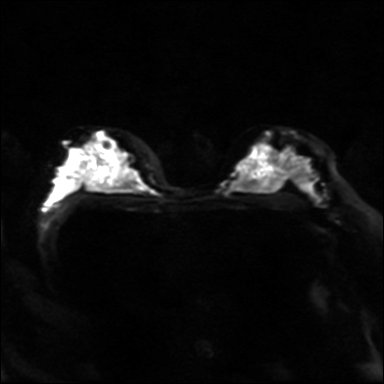
Breast MRI, one axial slice. Diffusion-weighted series; image 2 of 4 stored at this slice position (different b-values; order by instance number). 3 T. 4 mm slice thickness. 384 × 384 image matrix, field of view 320 × 320 mm. Female patient.
Outlined on this slice (manually delineated by an expert):
- tumour on diffusion-weighted imaging: bounding box (x1, y1, x2, y2) in pixels: (97, 132, 104, 141)